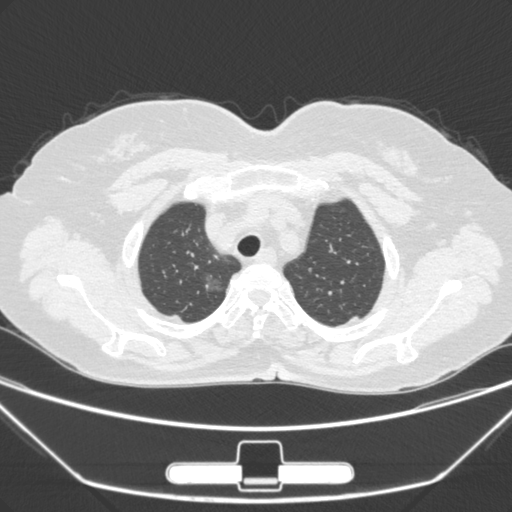
Chest CT, one axial slice. Slice 234 of 275 in the series (ordered by position). Lung window (W 1500 / L -600 HU). 1 mm slice thickness. 512 × 512 image matrix, field of view 356 × 356 mm. Female patient, age 63 years. From the clinical record (not read from this slice): clinical TNM (as recorded): T1a N0 M0; histopathological grade: G1.
Structures marked on this image (rectangle marked by the reading radiologist):
- lung tumour (recorded histology: adenocarcinoma): bounding box [x1, y1, x2, y2] px = [196, 271, 227, 303]